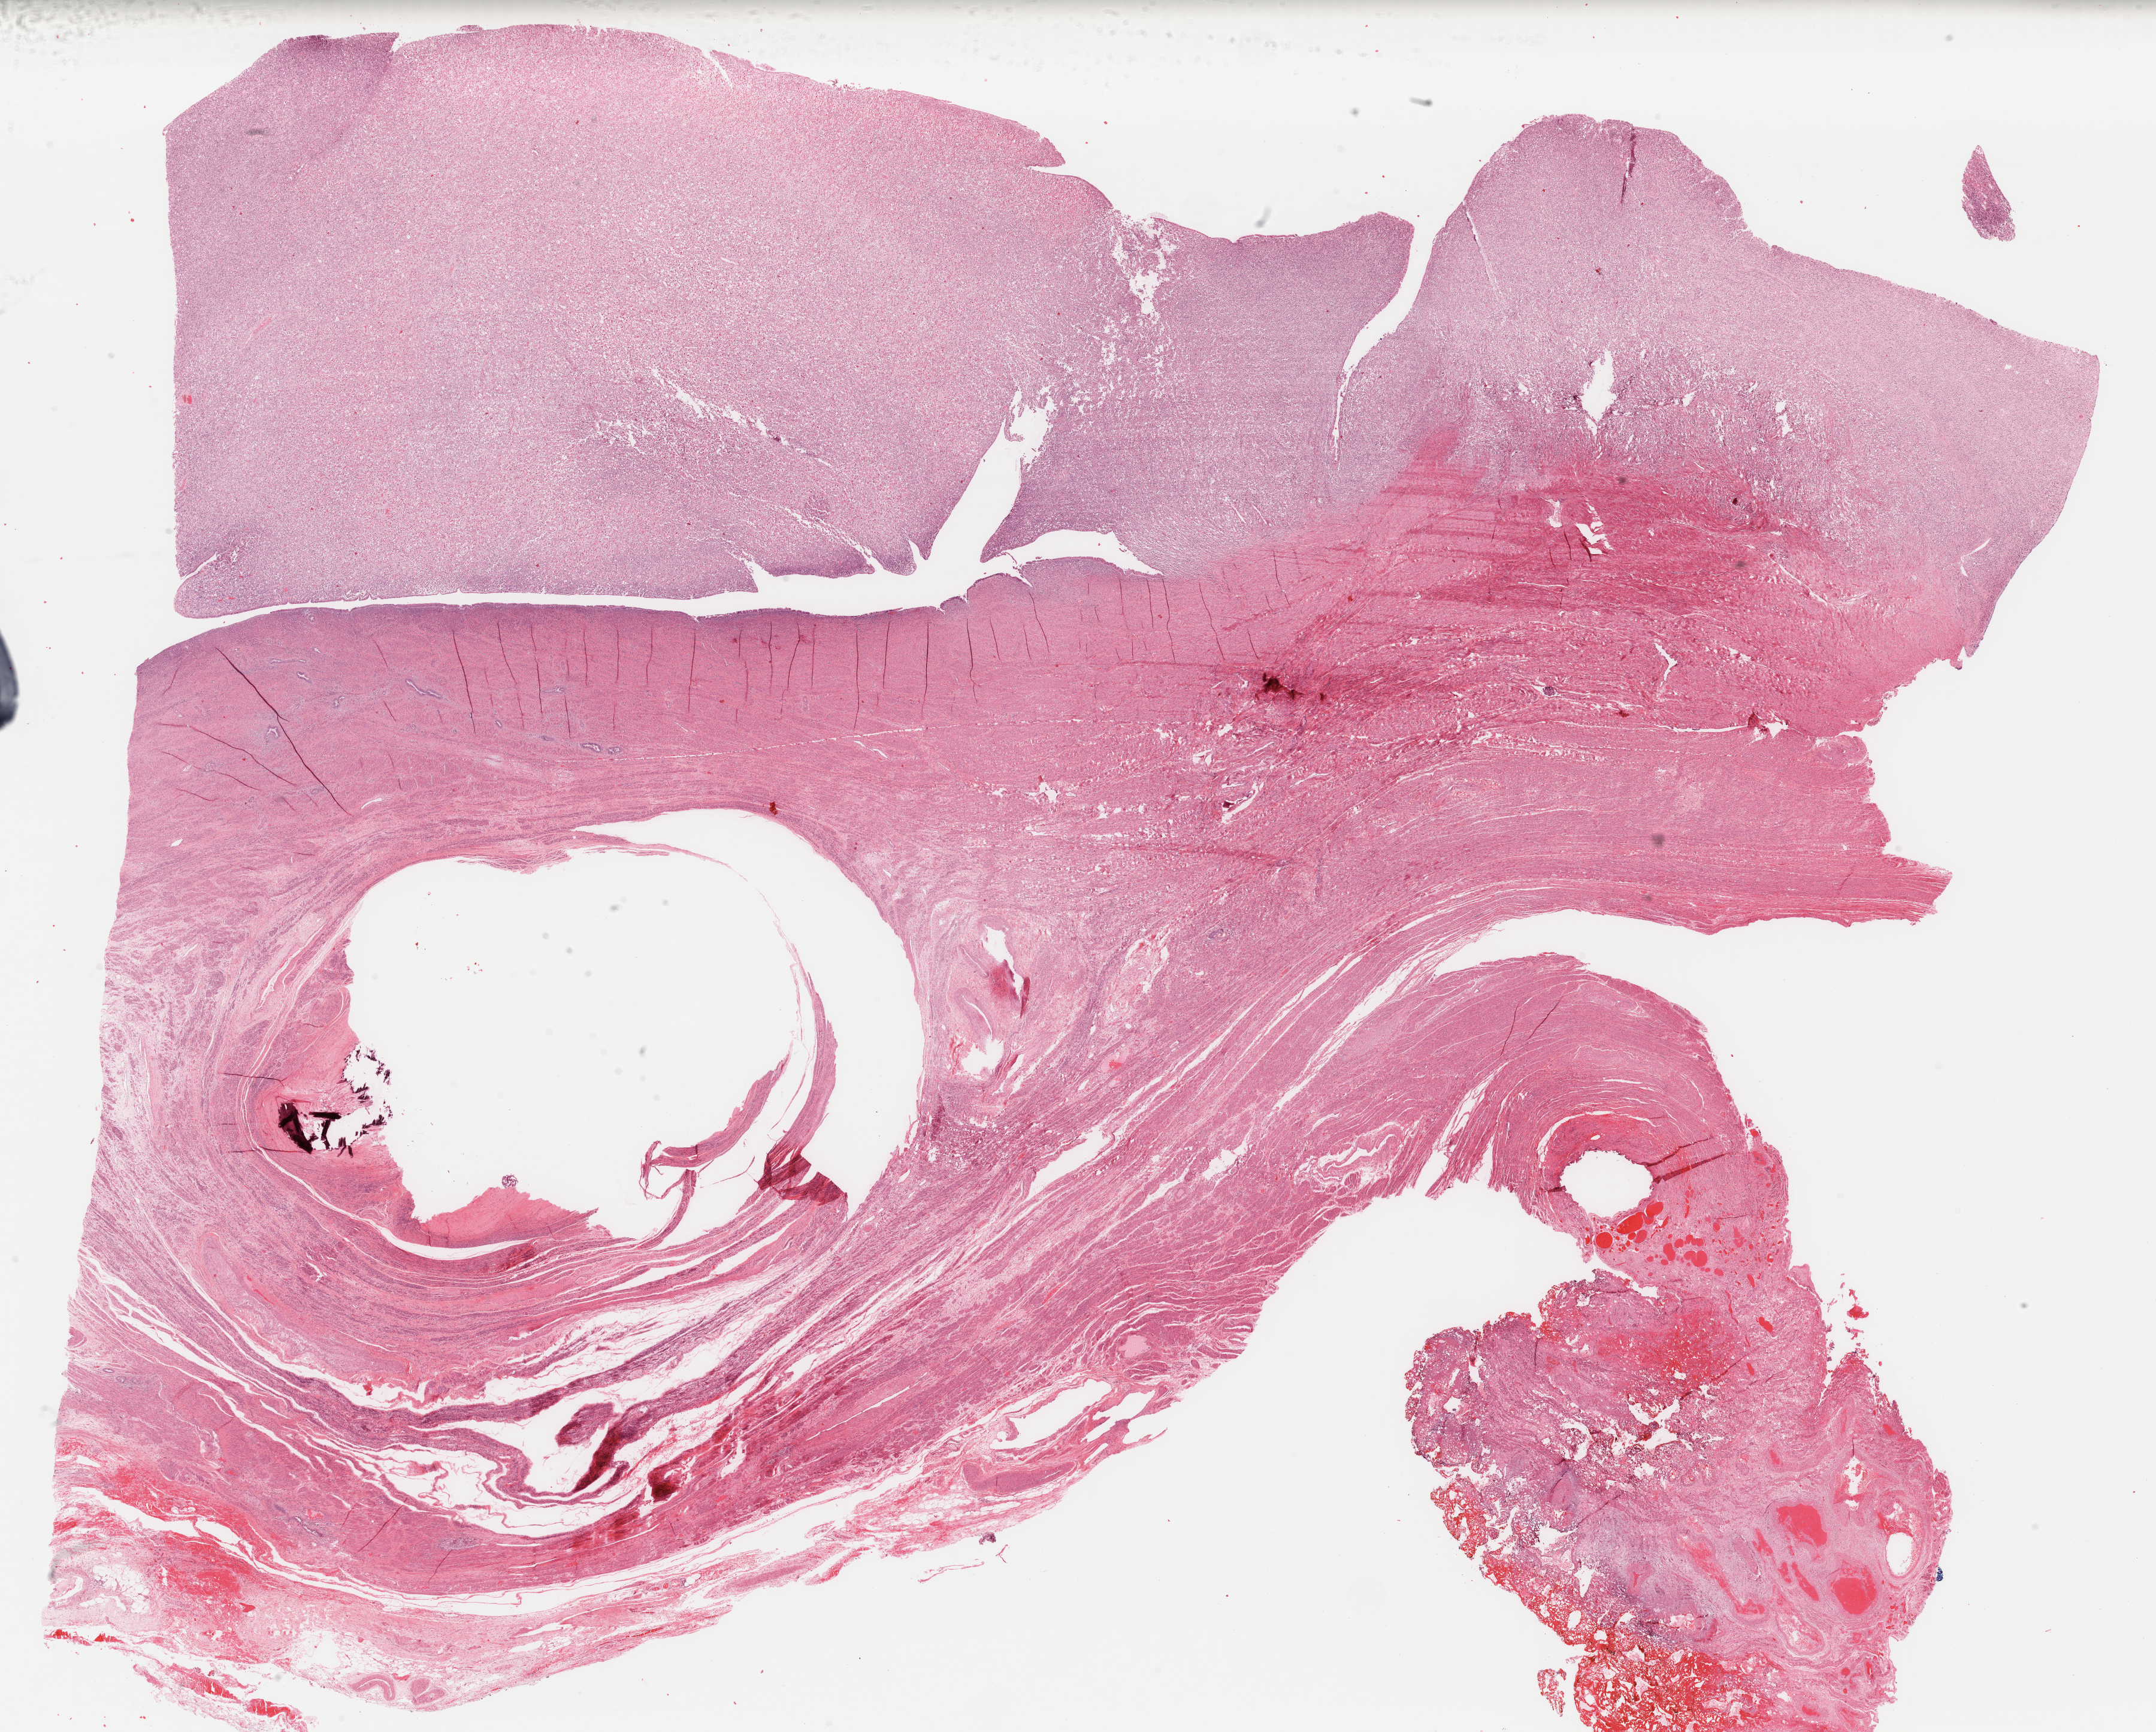
Whole-slide histology image, Hematoxylin and eosin (H&E) stained, a low-resolution overview of the entire scanned area, about 28.4 x 22.8 mm. FFPE section. Sample: primary tumour, uterus. Patient: female, age at initial diagnosis 87 years.
Pathologic diagnosis: Mullerian mixed tumor.